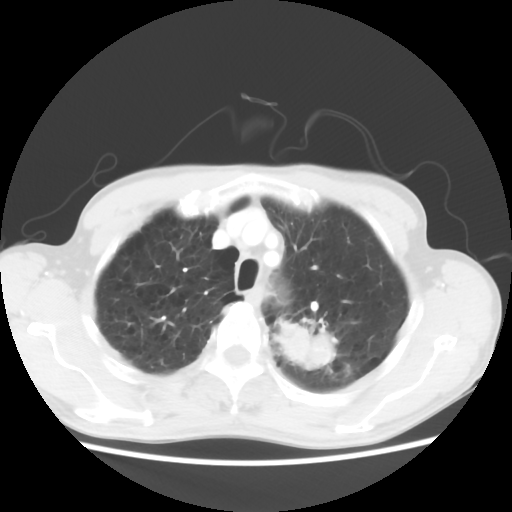
Chest CT, one axial slice; slice 51 of 64 in the series (ordered by position); reconstruction kernel STANDARD; 120 kVp; lung window (W 1500 / L -600 HU); 512 × 512 image matrix, field of view 346 × 346 mm. Patient: male, 63 years. Case-level facts recorded for this patient, not image findings: clinical TNM (as recorded): T2 N0 M0.
Structures marked on this image (bounding box drawn by a radiologist):
- lung tumour (recorded histology: adenocarcinoma): bounding box <272,314,344,374> (left, top, right, bottom; pixels)